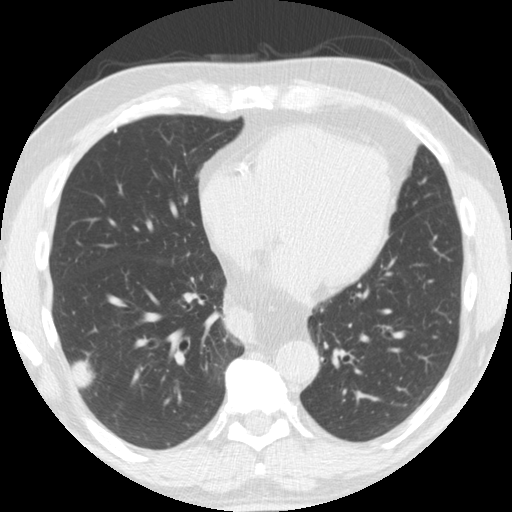
Low-dose screening chest CT, one axial slice; position 69 of 174 along the scan axis; reconstruction kernel STANDARD; lung window (W 1500 / L -600 HU); 2.5 mm slice thickness; 512 × 512 image matrix.
Outlined on this slice (outlined manually by an expert reader):
- lesion 1 (tumor, lower lobe of right lung): bounding box <72,360,94,388> (left, top, right, bottom; pixels)